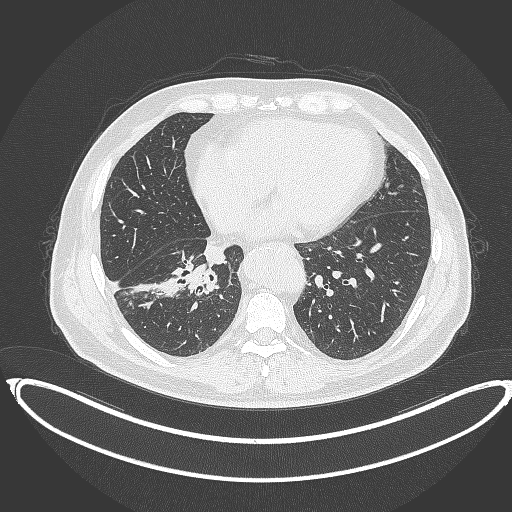
Chest CT, one axial slice; slice 149 of 387 in the series (ordered by position); reconstruction kernel B70f; 120 kVp; lung window (W 1500 / L -600 HU); 512 × 512 image matrix, field of view 448 × 448 mm. Male patient, age 61 years. From the clinical record (not read from this slice): clinical TNM (as recorded): T1b N1 M0.
Annotated regions visible in this slice (bounding box drawn by a radiologist):
- lung tumour (recorded histology: squamous cell carcinoma): bounding box (x1, y1, x2, y2) in pixels: (180, 257, 222, 295)